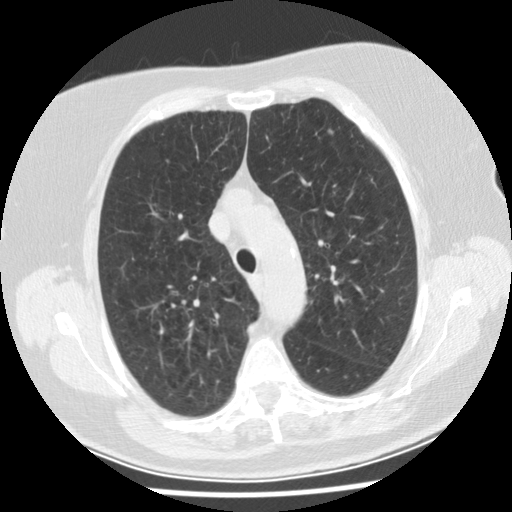
Chest CT (low-dose screening protocol), one axial image; first (baseline) screen; lung window (W 1500 / L -600 HU); slice 118 of 149 in the series. Female, age 74 years at enrolment. Former smoker at enrolment.
Lesion marked by an expert reader, bounding box (x1, y1, x2, y2) in pixels: (318, 121, 344, 147). The screening reader recorded 2 non-calcified nodules or masses ≥4 mm on this exam (left upper lobe, left lower lobe); which of them this box marks is not recorded. Official screen result: positive, change unspecified: nodule(s) >= 4 mm or enlarging nodule(s), mass(es), or other non-specific abnormalities suspicious for lung cancer.